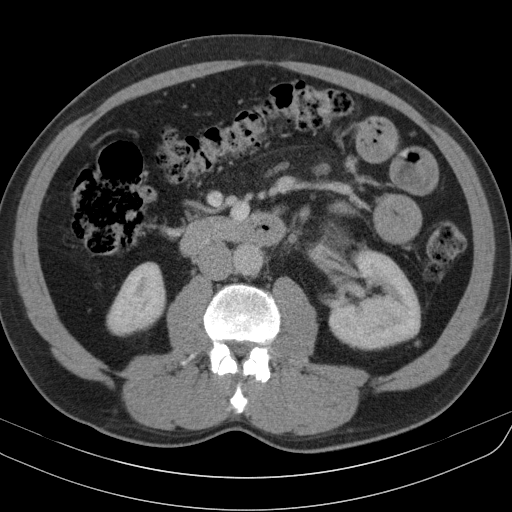
Contrast-enhanced abdominal CT, one axial slice. Slice 53 of 91 in the series (ordered by position). Reconstruction kernel B31s. 130 kVp. Soft-tissue window (W 400 / L 40 HU). 5 mm slice thickness. 512 × 512 image matrix, field of view 370 × 370 mm. Male patient, age 51 years. Case-level facts recorded for this patient, not image findings: diagnosis: adrenocortical carcinoma; tumour side: left adrenal; tumour size at pathology: 18 cm; Ki-67 index: 40 %; stage (as recorded): 3.
Structures marked on this image (semi-automatic segmentation, software-assisted and operator-edited):
- mass: bounding box <327,227,347,253> (left, top, right, bottom; pixels)